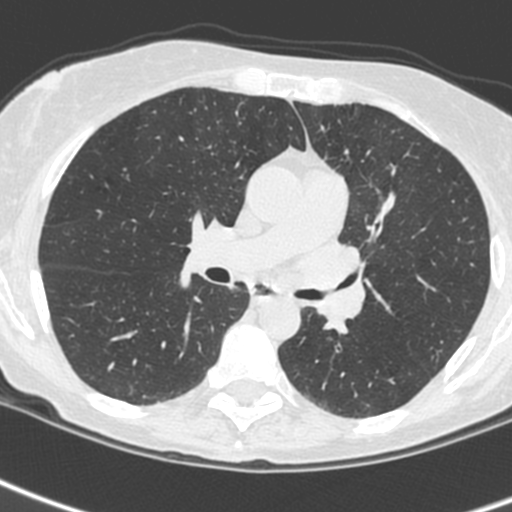
Low-dose screening chest CT, one axial slice; position 143 of 242 along the scan axis; 120 kVp; lung window (W 1500 / L -600 HU); 1.3 mm slice thickness; 512 × 512 image matrix.
Outlined on this slice (manually delineated by an expert):
- lesion 3 (tumor, upper lobe of left lung): bounding box (x1, y1, x2, y2) in pixels: (294, 236, 365, 322)